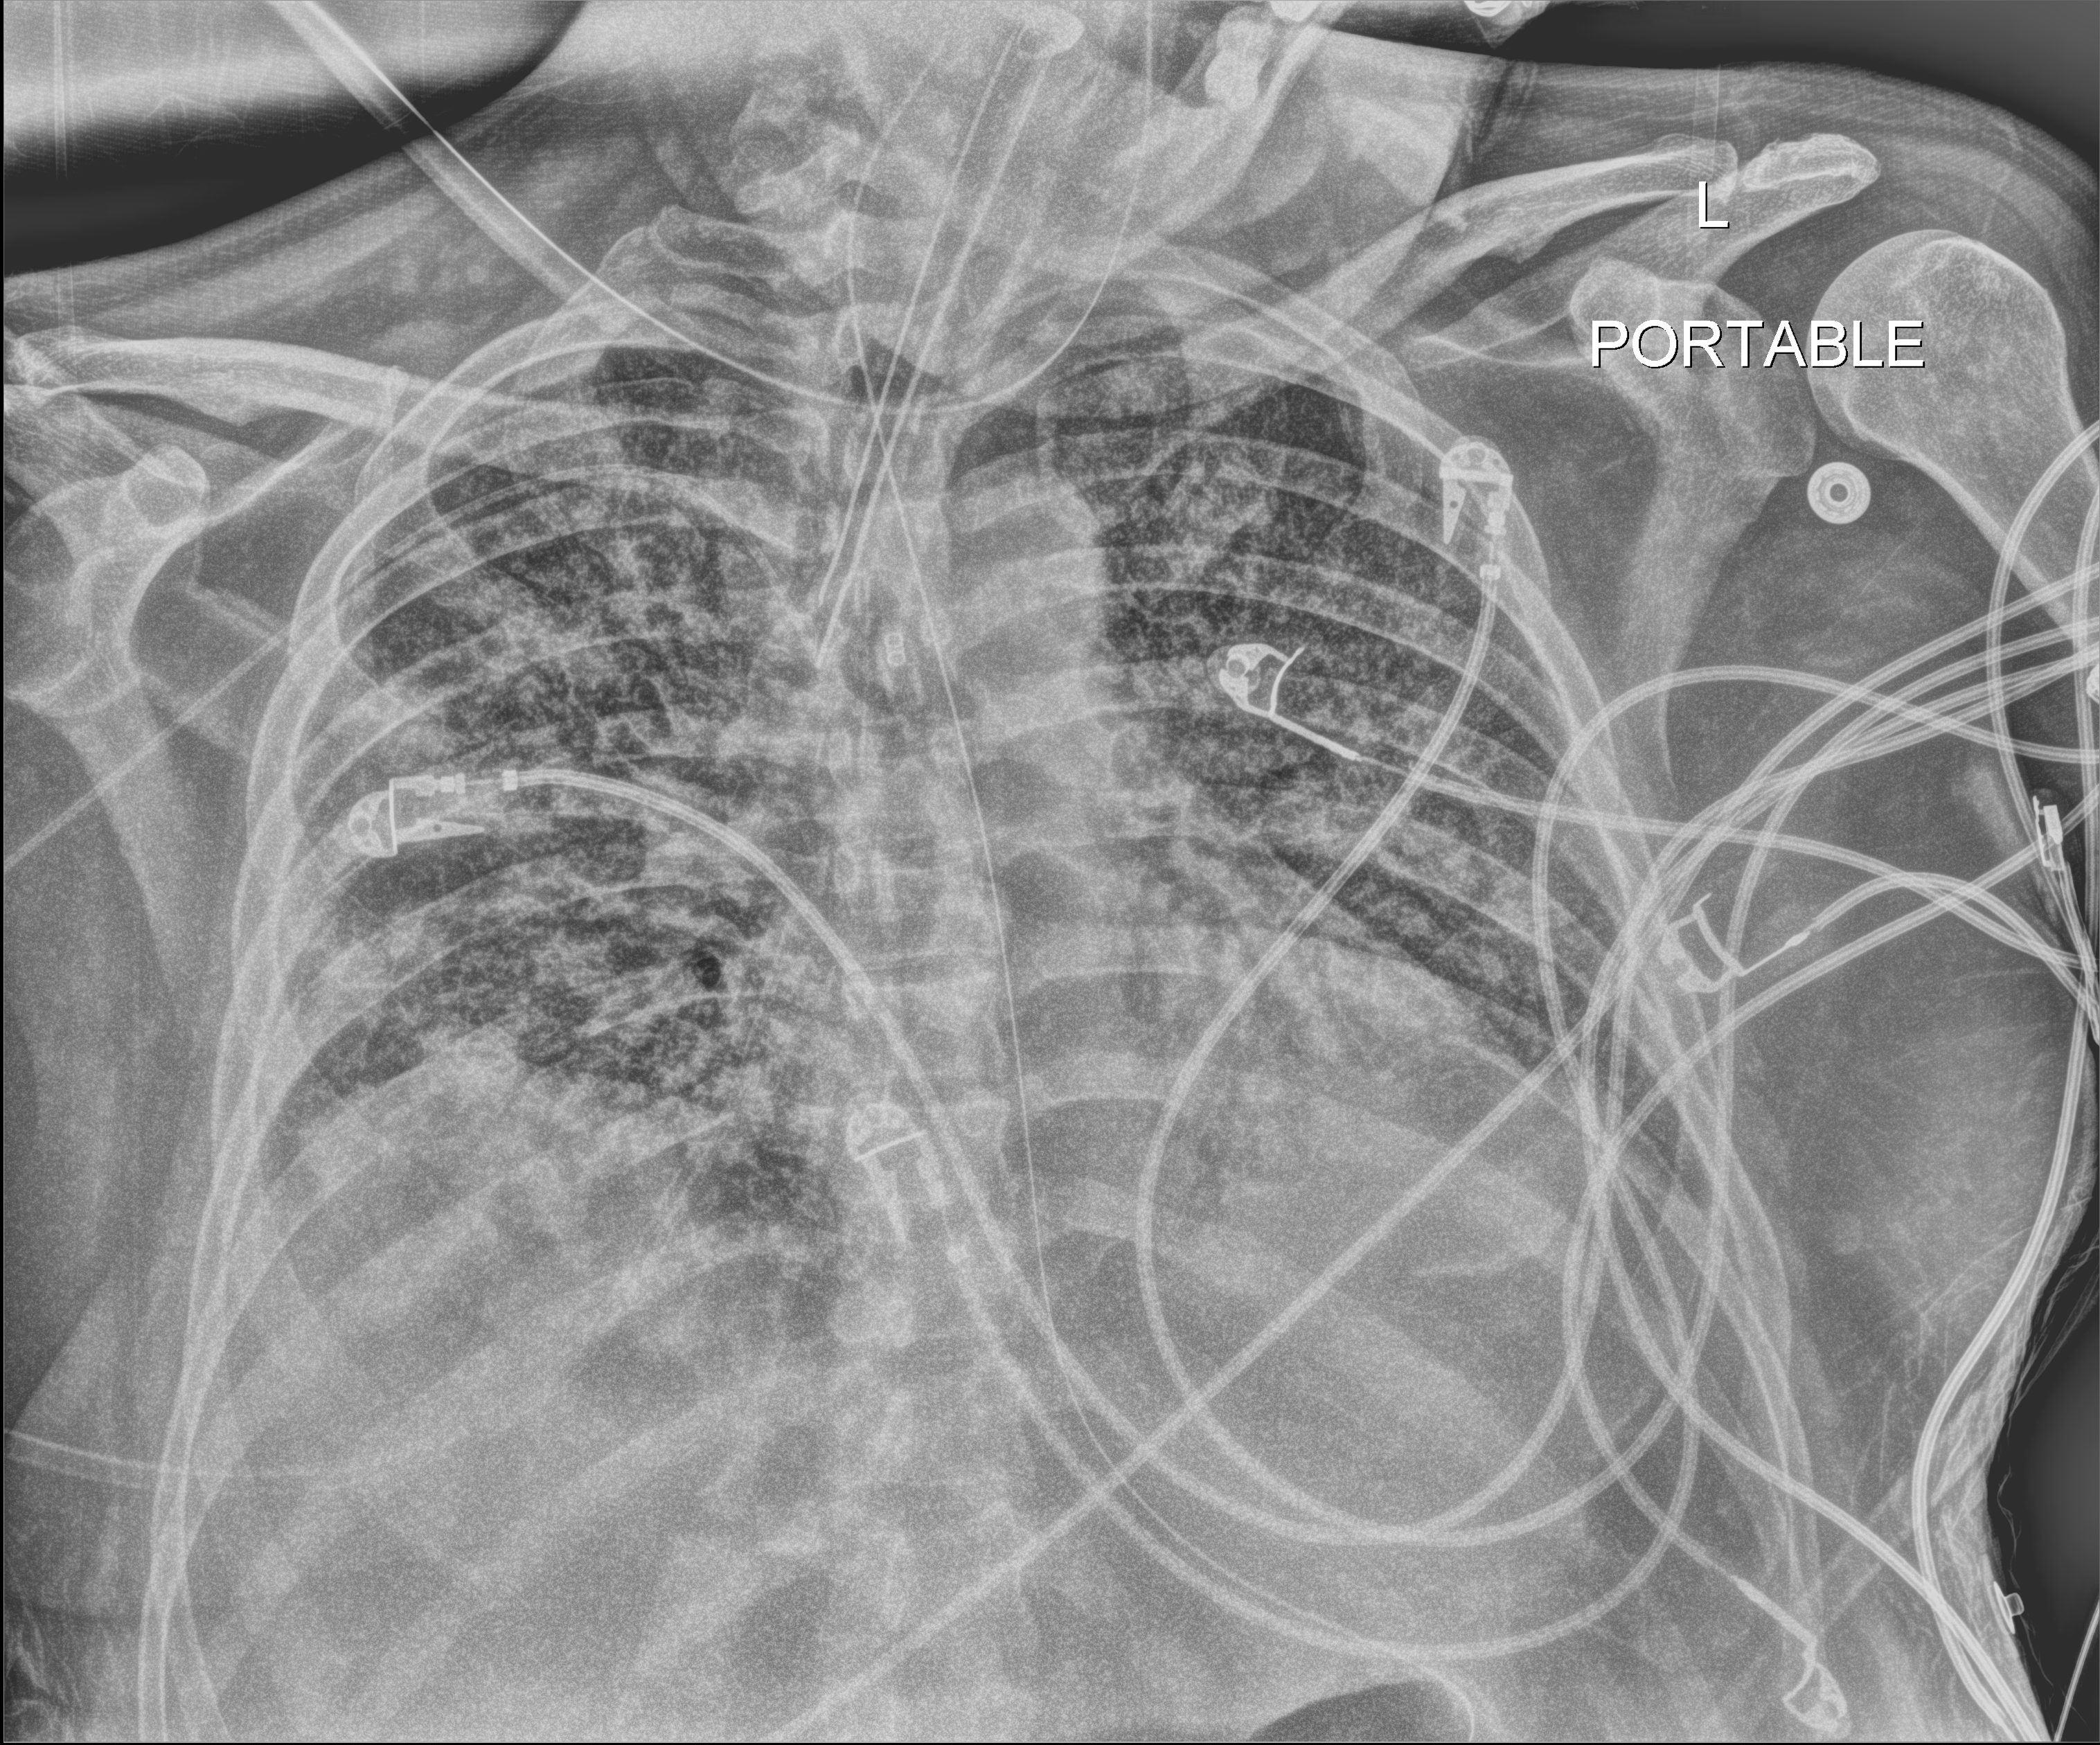
Chest X-ray (portable); anteroposterior (AP) projection. Male patient hospitalised with COVID-19, age 18–59 years.
Hospital-stay facts (about this admission, not read from this image; timing relative to this image not recorded): admitted to intensive care during this hospital stay: yes; mechanically ventilated during this hospital stay: yes; length of hospital stay: 96 days.